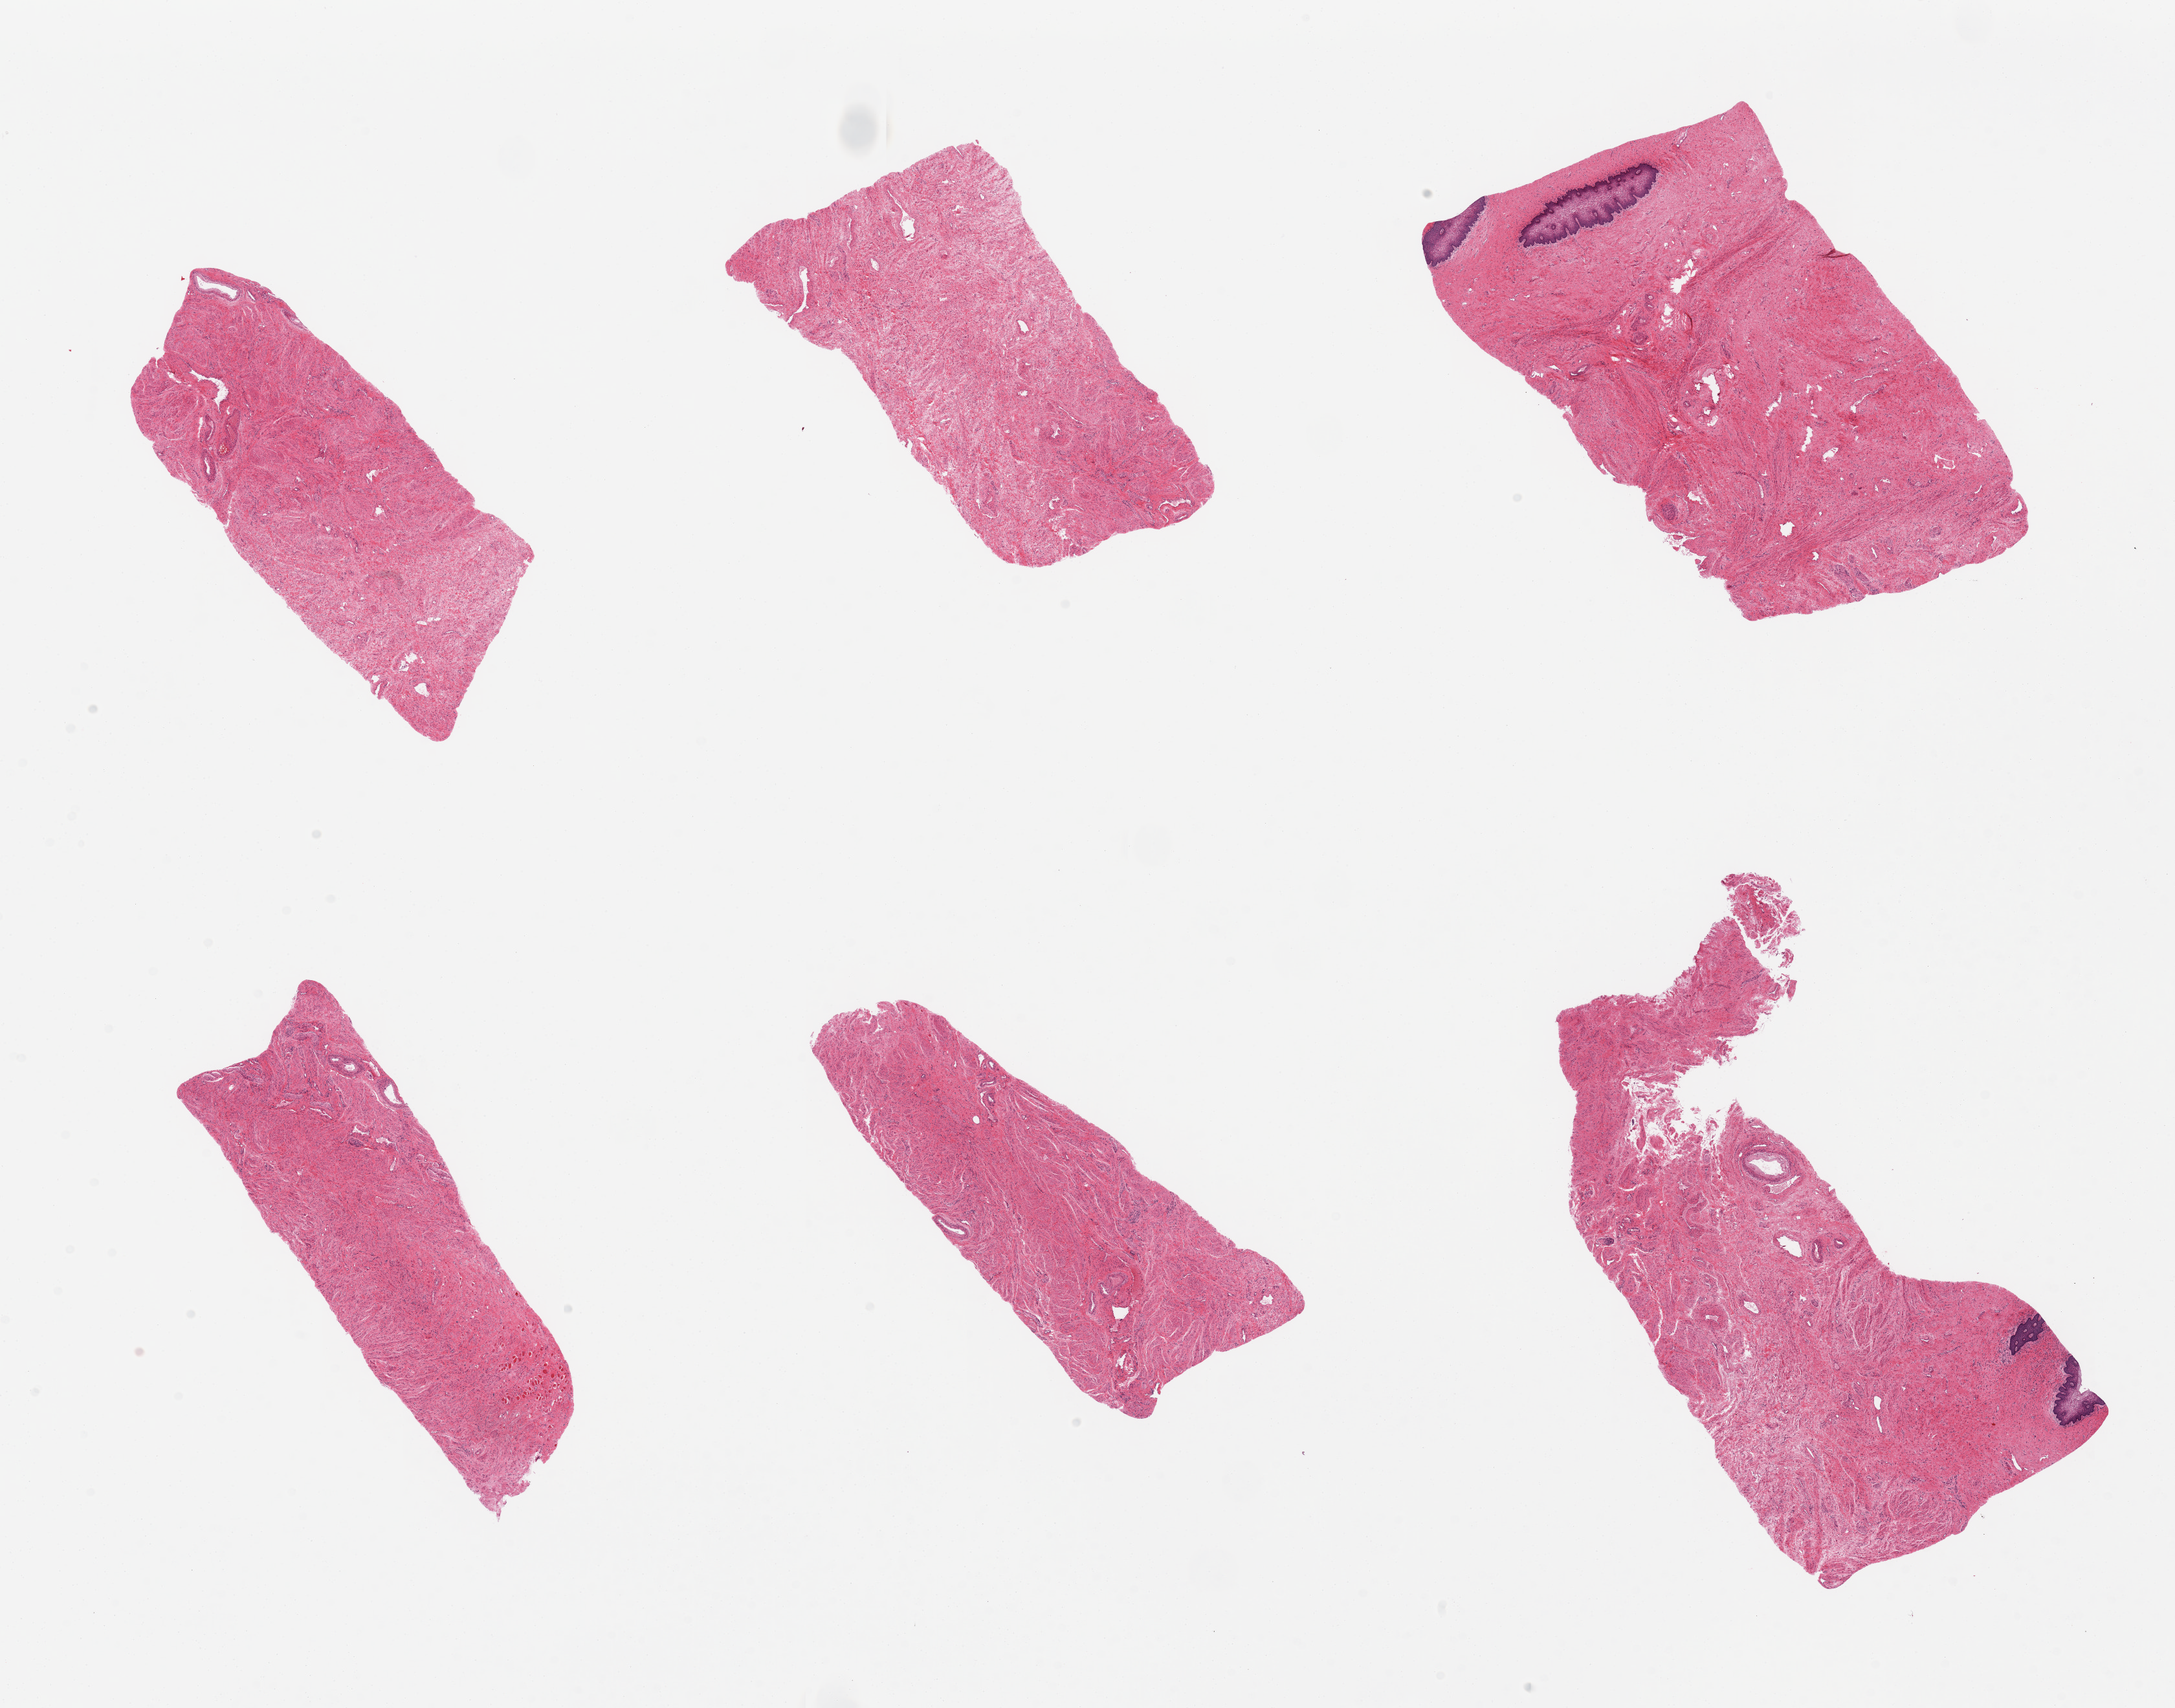
Digitized H&E-stained section, a low-resolution overview of the entire scanned area, about 26.6 x 20.9 mm (from a 20x scan); PAXgene-fixed, paraffin-embedded tissue; target tissue: vagina; donor tissue sample. Donor sex: female.
Review note (as recorded): 6 pieces, only 2 pieces include squamous epithelium (5-10%).